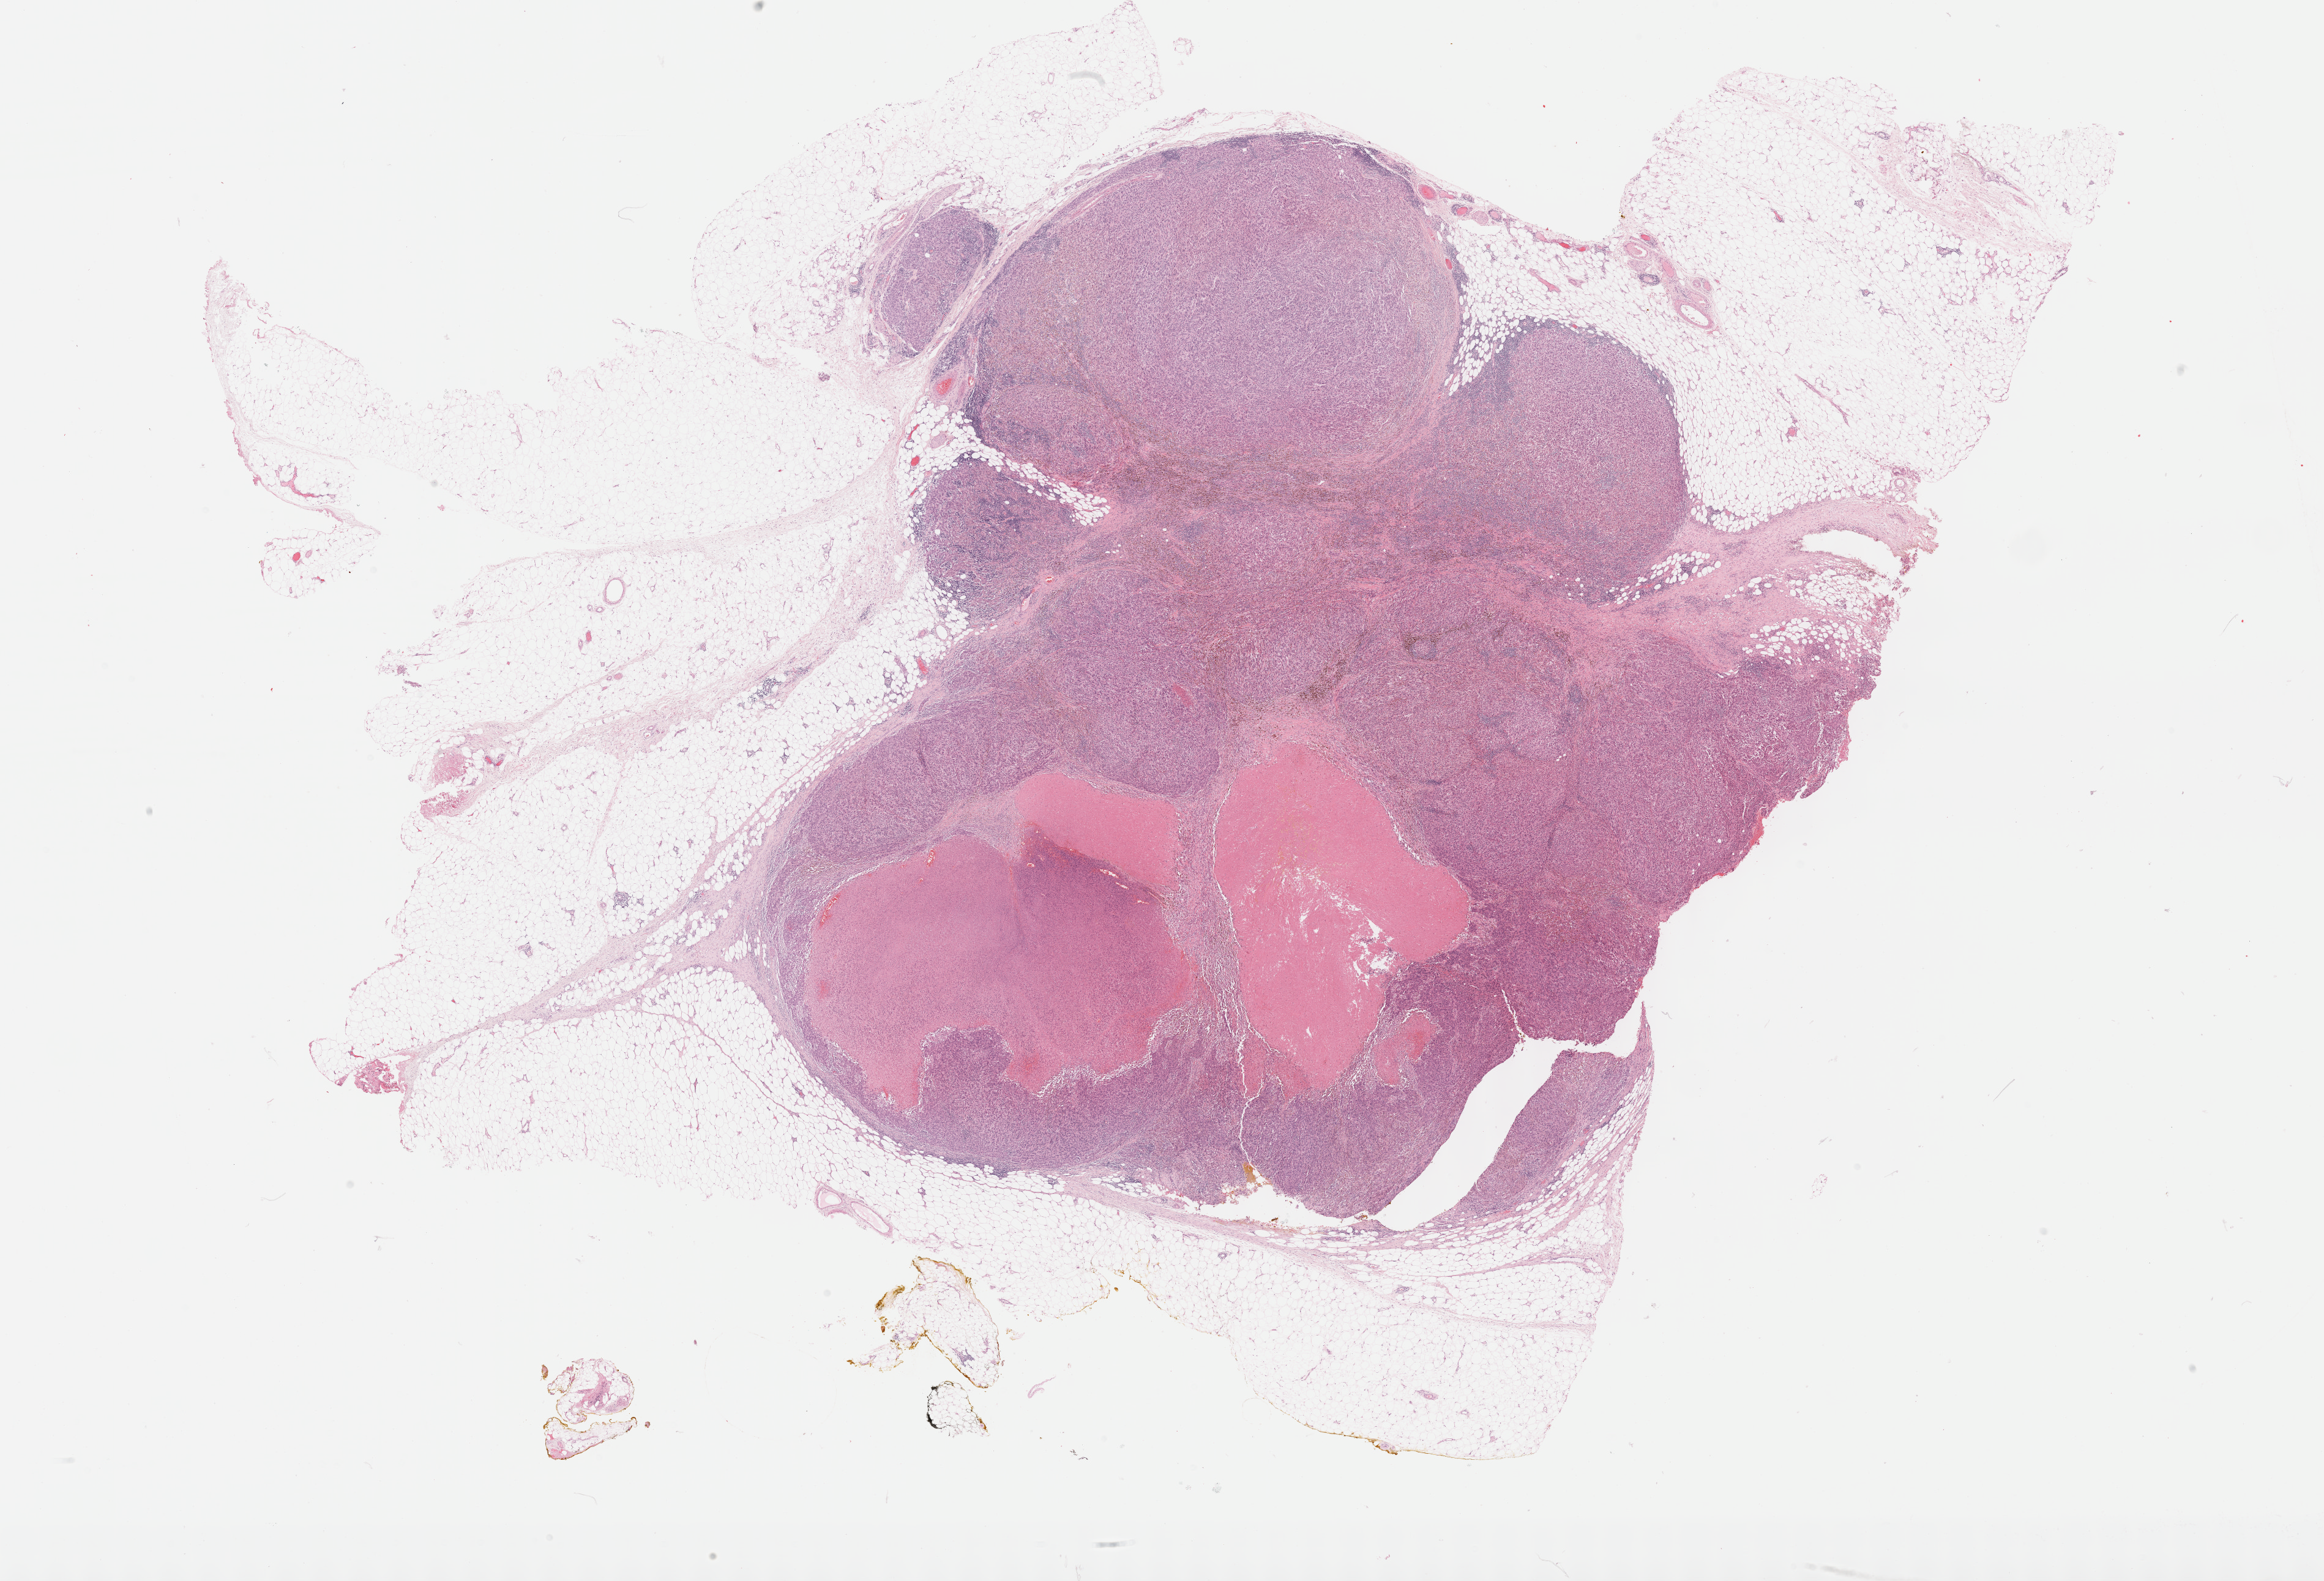
Whole-slide histology image, H&E-stained — shown as a low-resolution overview of the whole scanned area (about 30.7 x 20.9 mm, slide scanned at 40x); formalin-fixed paraffin-embedded (FFPE) diagnostic section; metastatic tumour sample, sampled site: connective, subcutaneous and other soft tissues of lower limb and hip. Male patient; age at initial diagnosis 74 years.
- this section: metastatic tumour tissue
- patient diagnosis: Superficial spreading melanoma